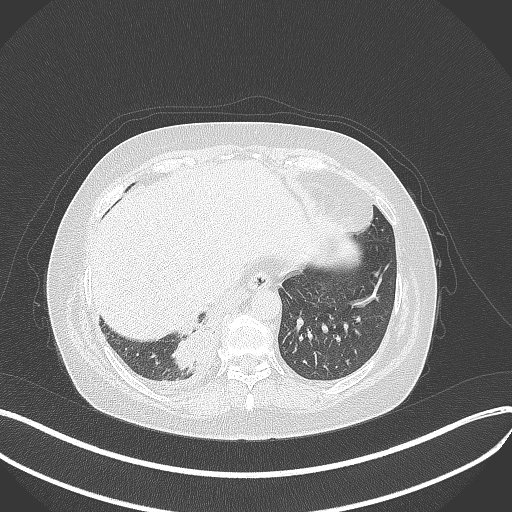
Chest CT, one axial slice; slice 87 of 381 in the series (ordered by position); reconstruction kernel B70f; lung window (W 1500 / L -600 HU); 512 × 512 image matrix, field of view 400 × 400 mm. Patient: female, 56 years. Case-level facts recorded for this patient, not image findings: clinical TNM (as recorded): T2b N1 M0; histopathological grade: G3.
Outlined on this slice (rectangle marked by the reading radiologist):
- lung tumour (recorded histology: small cell carcinoma): bounding box (x1, y1, x2, y2) in pixels: (169, 331, 219, 371)